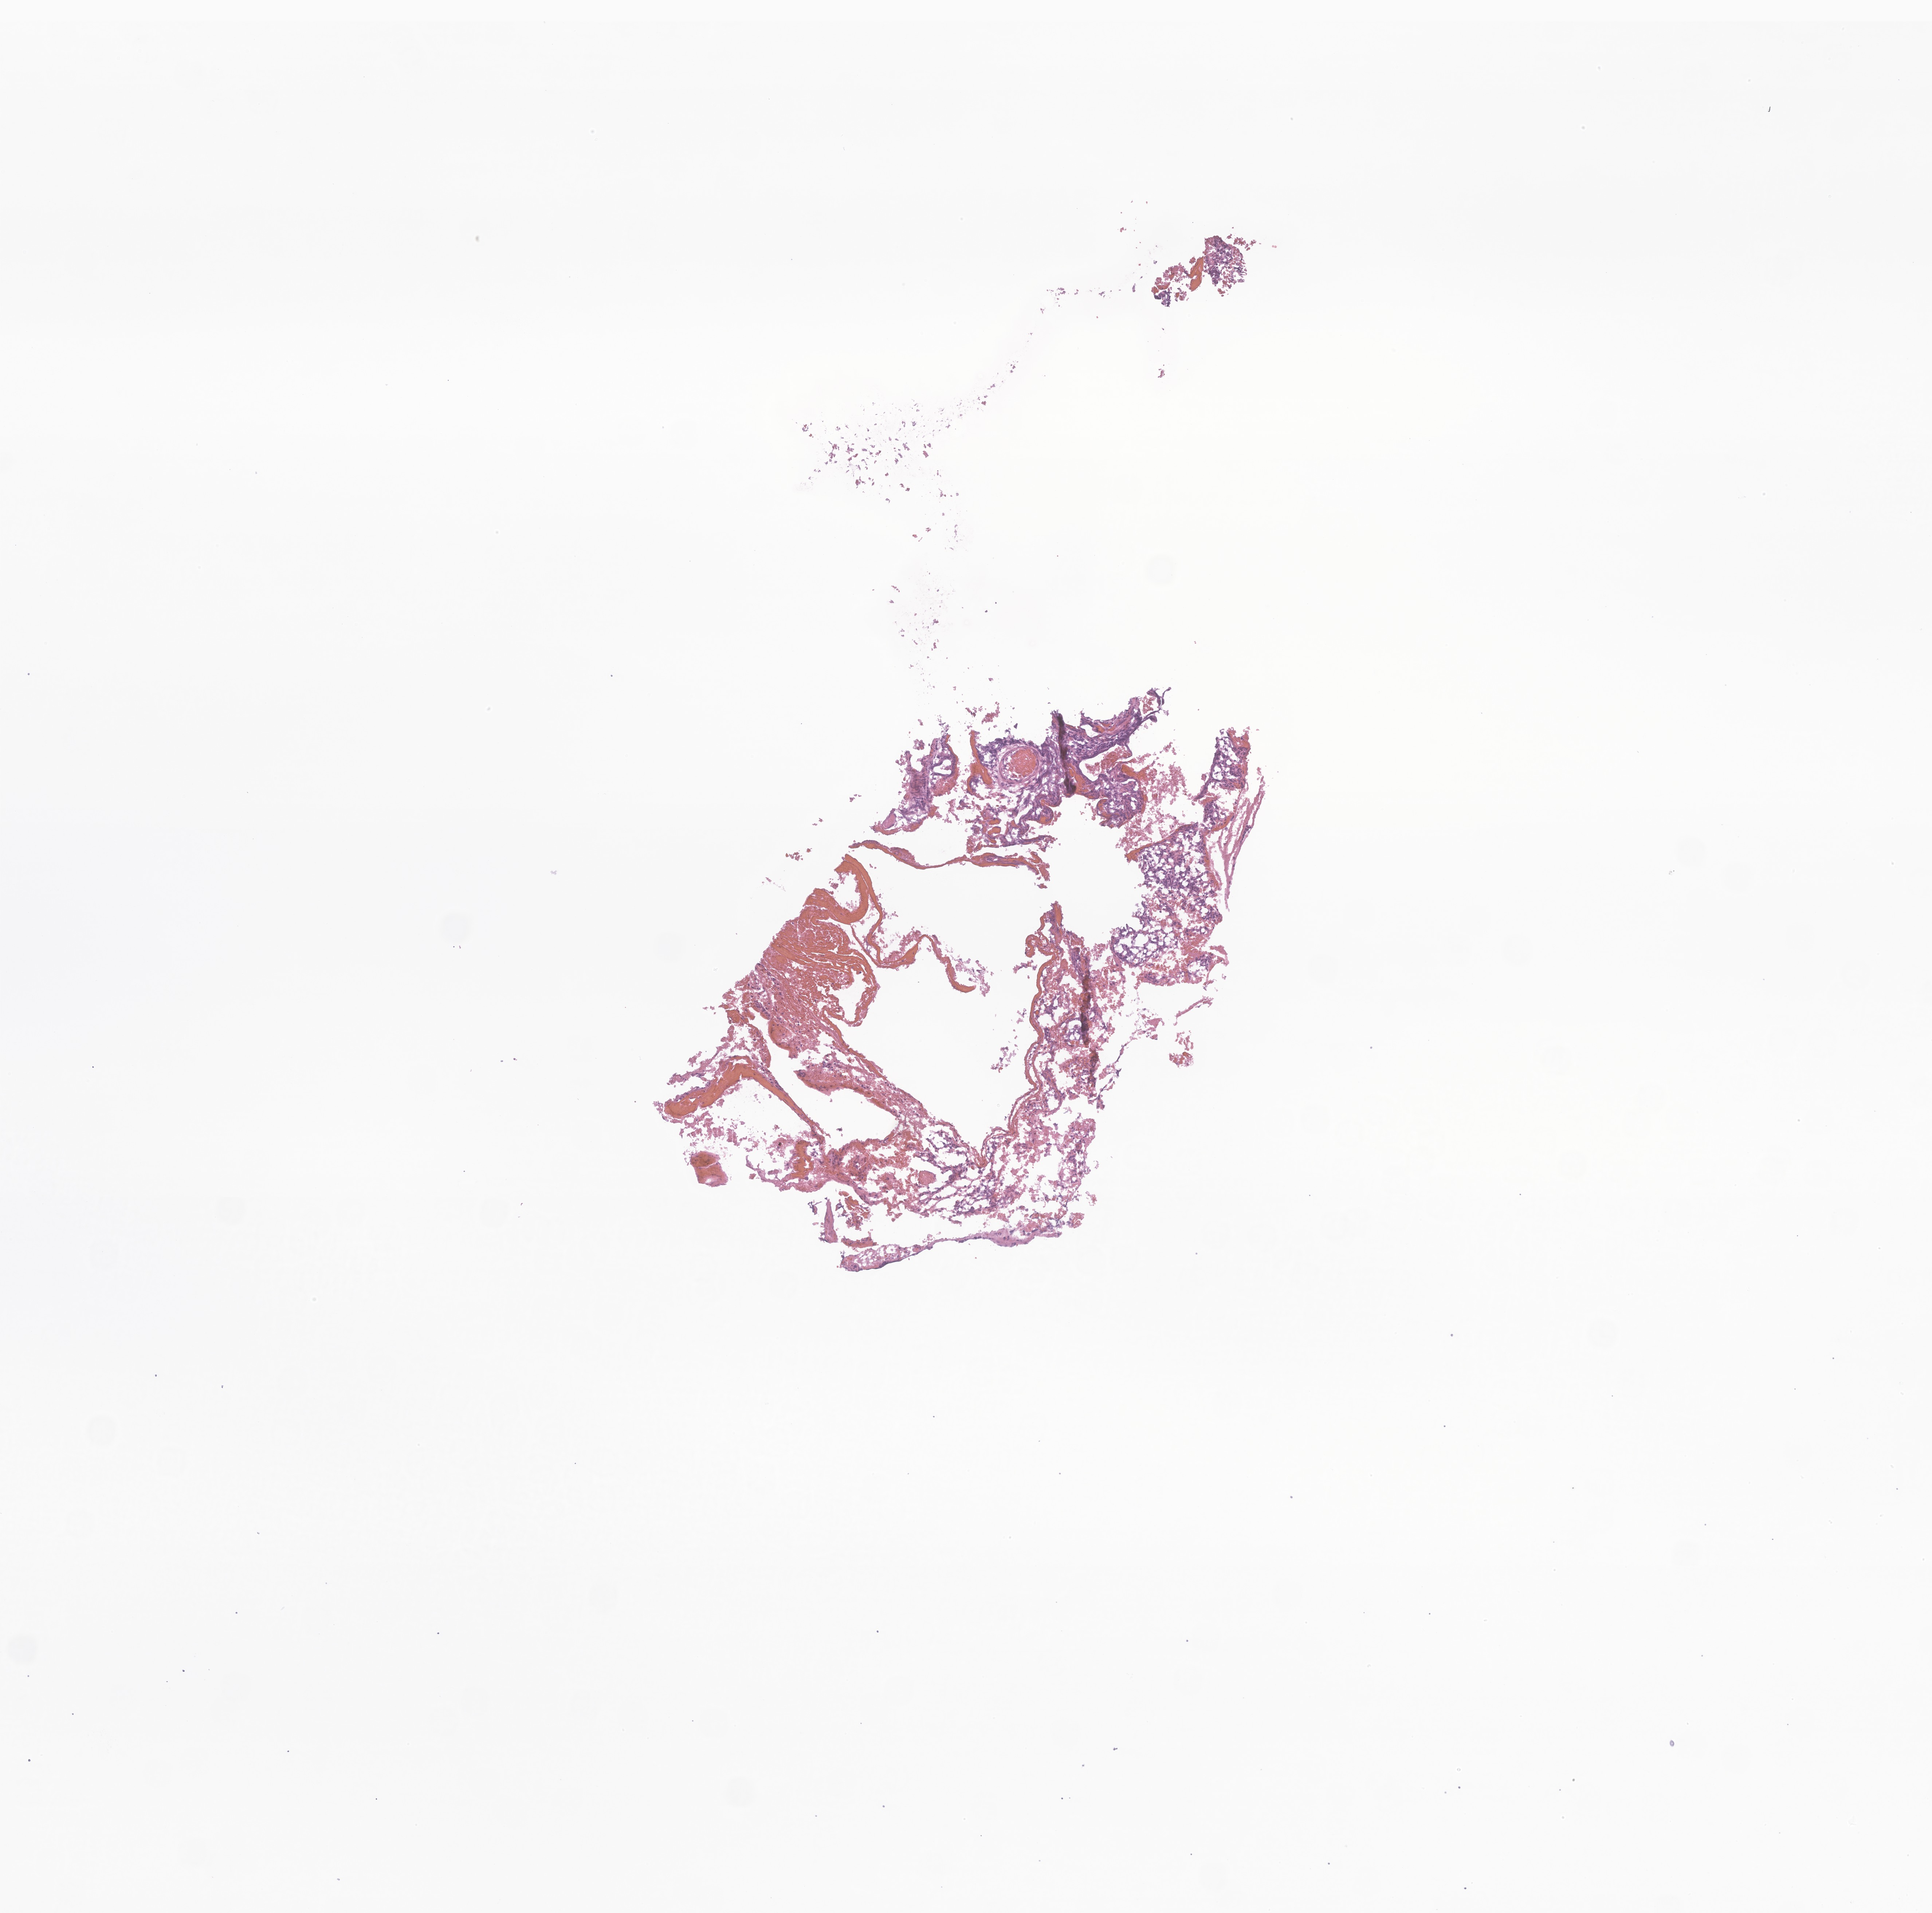
Whole-slide image, hematoxylin and eosin (H&E) stain of tumor tissue from the brain — low-resolution overview of the scanned area, about 5.6 x 5.5 mm; frozen section (OCT-embedded). Patient: male, age 766 days (about 2.1 years).
Diagnosis (ICD-O-3 morphology term): Neoplasm, uncertain whether benign or malignant.